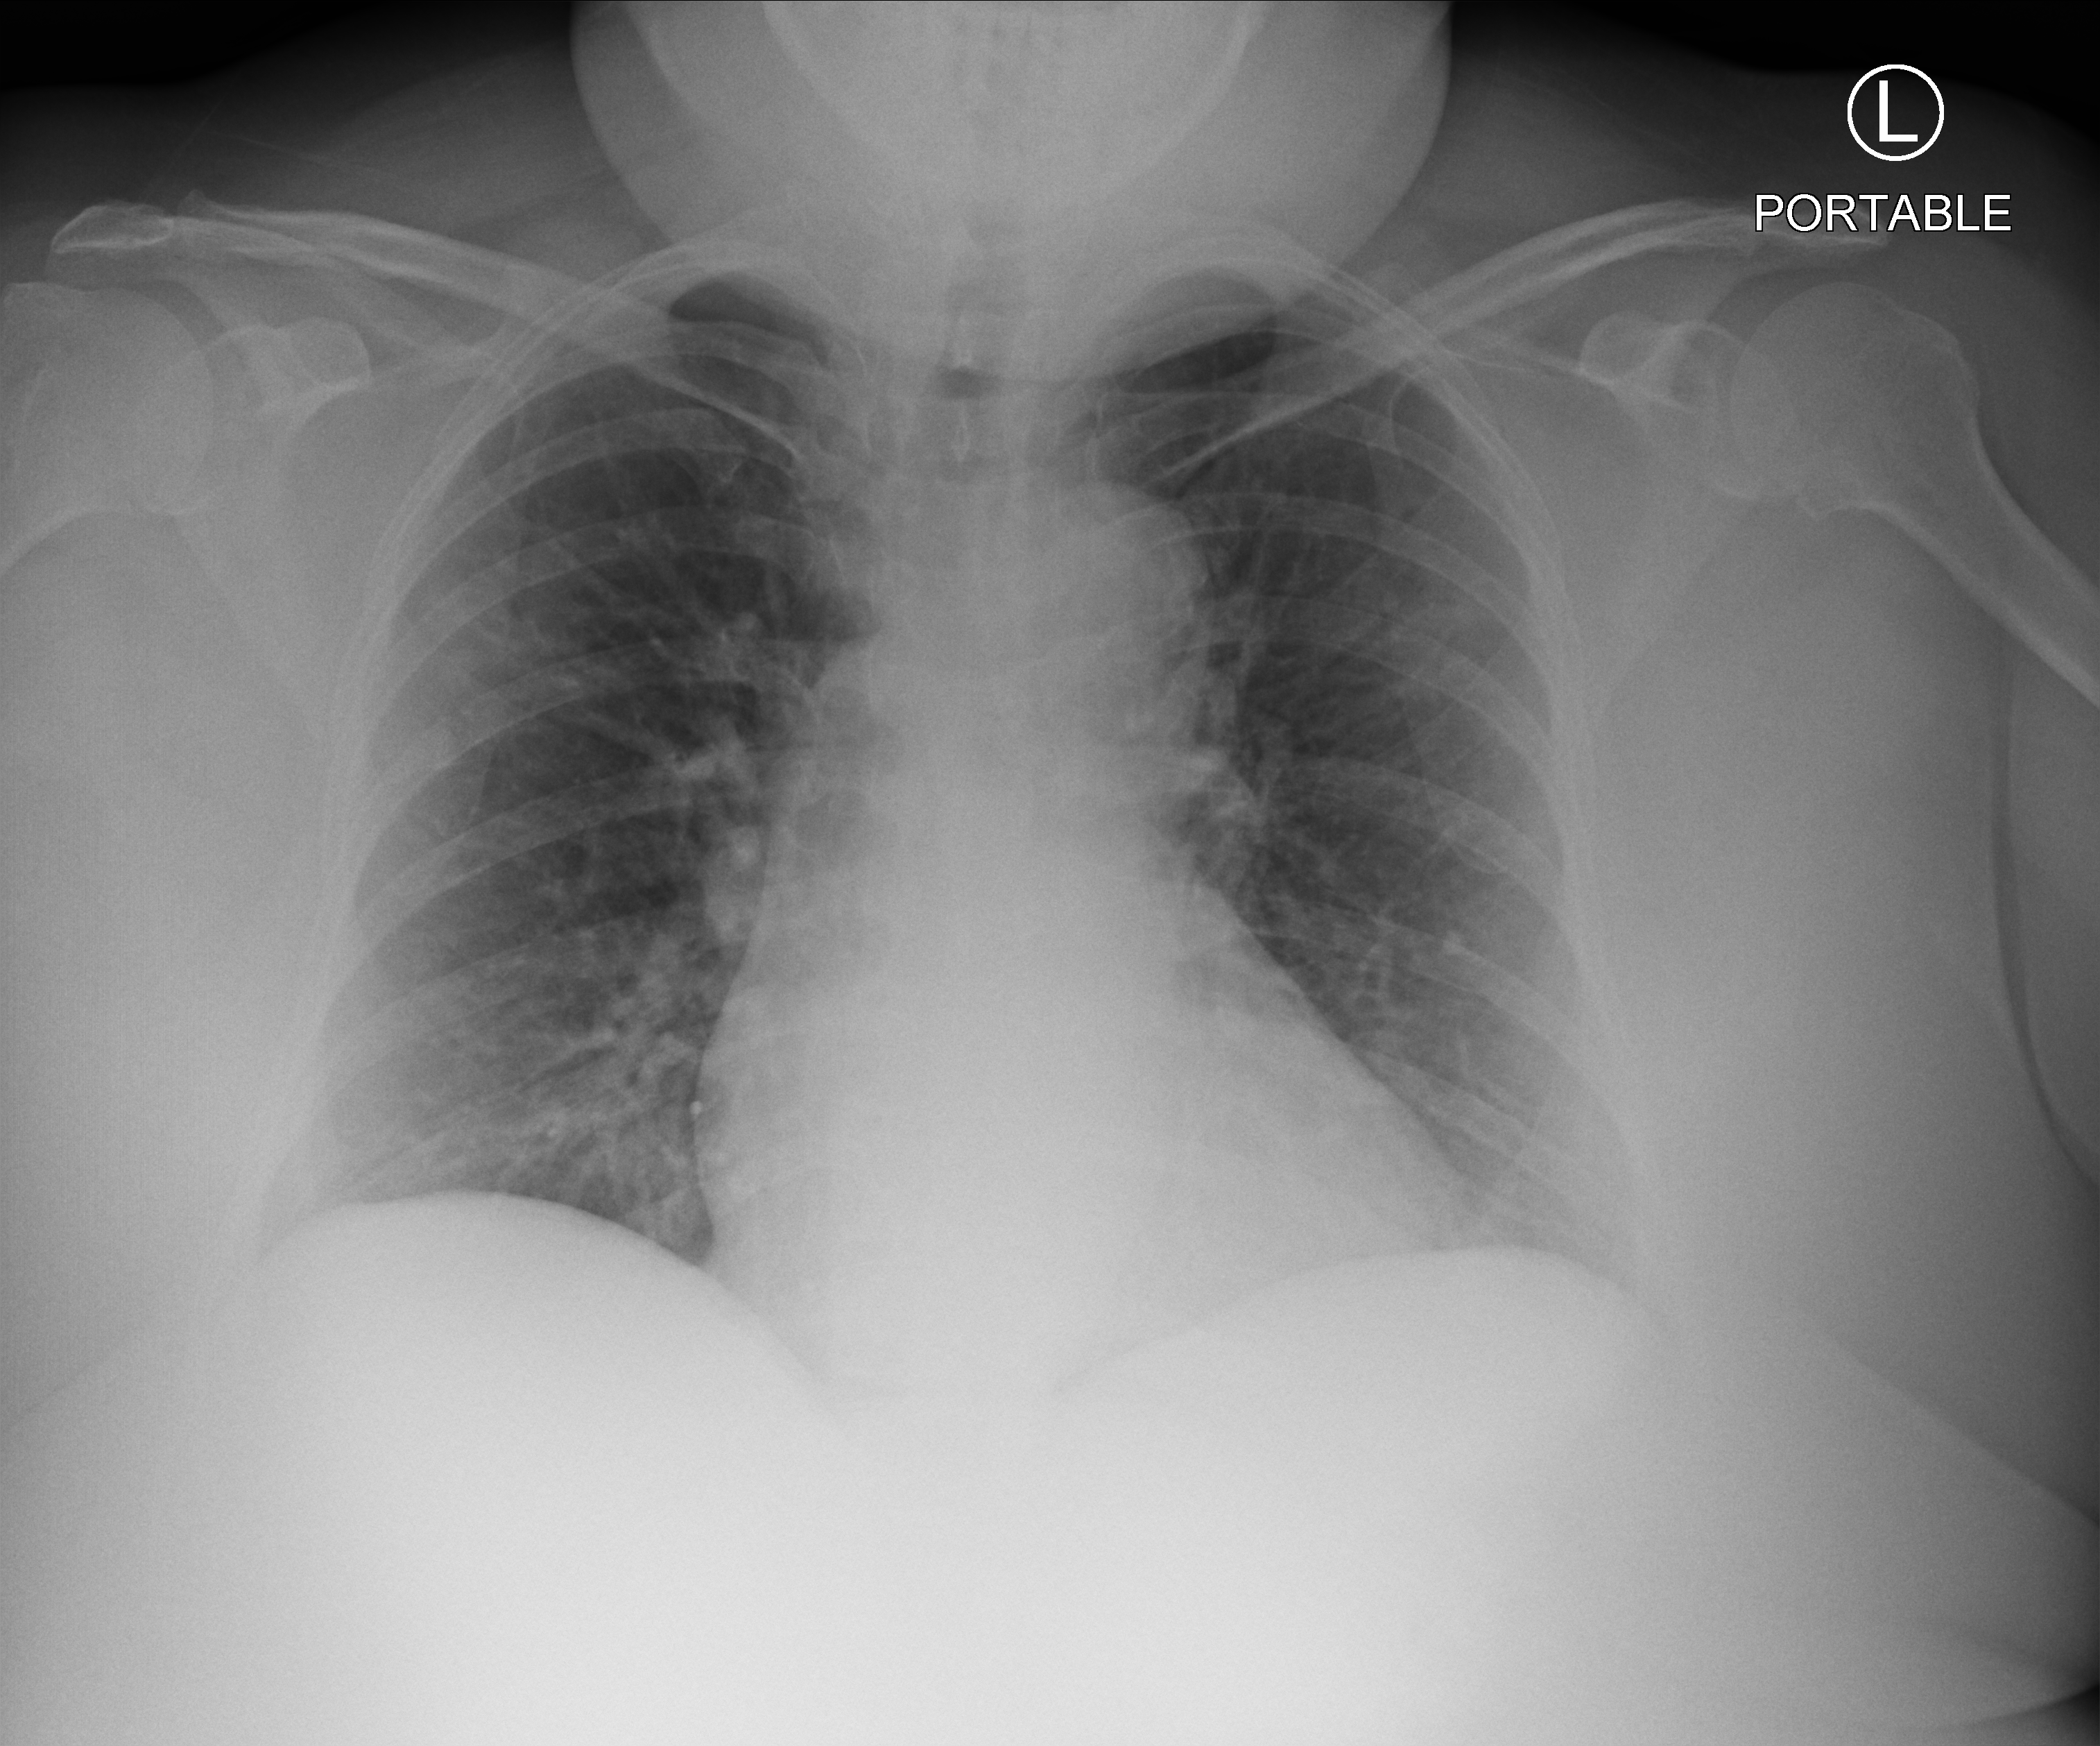
Bedside chest radiograph (computed radiography); anteroposterior (AP) projection. Female patient hospitalised with COVID-19, age 18–59 years.
Hospital-stay facts (about this admission, not read from this image; timing relative to this image not recorded):
- chronic kidney disease (admission record): no
- smoking status (admission record): never
- mechanically ventilated during this hospital stay: no